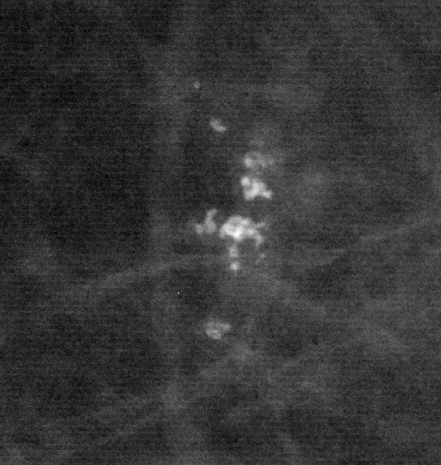
Cropped region of a digitized screen-film mammogram centred on a radiologist-marked abnormality, right breast, CC view.
Marked abnormality: calcifications, morphology pleomorphic, distribution clustered; BI-RADS assessment category 4; subtlety rating 5 on a 1 (subtle) to 5 (obvious) scale; pathology (as recorded): benign.